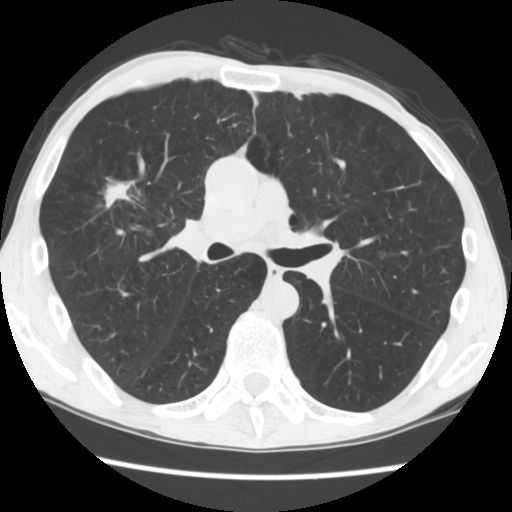
Axial slice from a low-dose chest CT screening exam, second screening round (one year after baseline), lung window (W 1500 / L -600 HU), 2.5 mm slice thickness, standard (soft-tissue) reconstruction kernel (STANDARD), slice 79 of 181 in the series. Male participant, aged 56 years at enrolment.
• Lesion marked by an expert reader, bounding box (x1, y1, x2, y2) in pixels: (91, 172, 146, 230).
• The screening reader recorded 2 non-calcified nodules or masses ≥4 mm on this exam (right upper lobe, left upper lobe); which of them this box marks is not recorded.
• Official screen result: positive, change unspecified: nodule(s) >= 4 mm or enlarging nodule(s), mass(es), or other non-specific abnormalities suspicious for lung cancer.
• Lung cancer was diagnosed 101 days after this screen: squamous cell carcinoma, NOS, right upper lobe, right middle lobe, well differentiated (G1), stage IA (AJCC 6th edition), 27 mm at pathology.